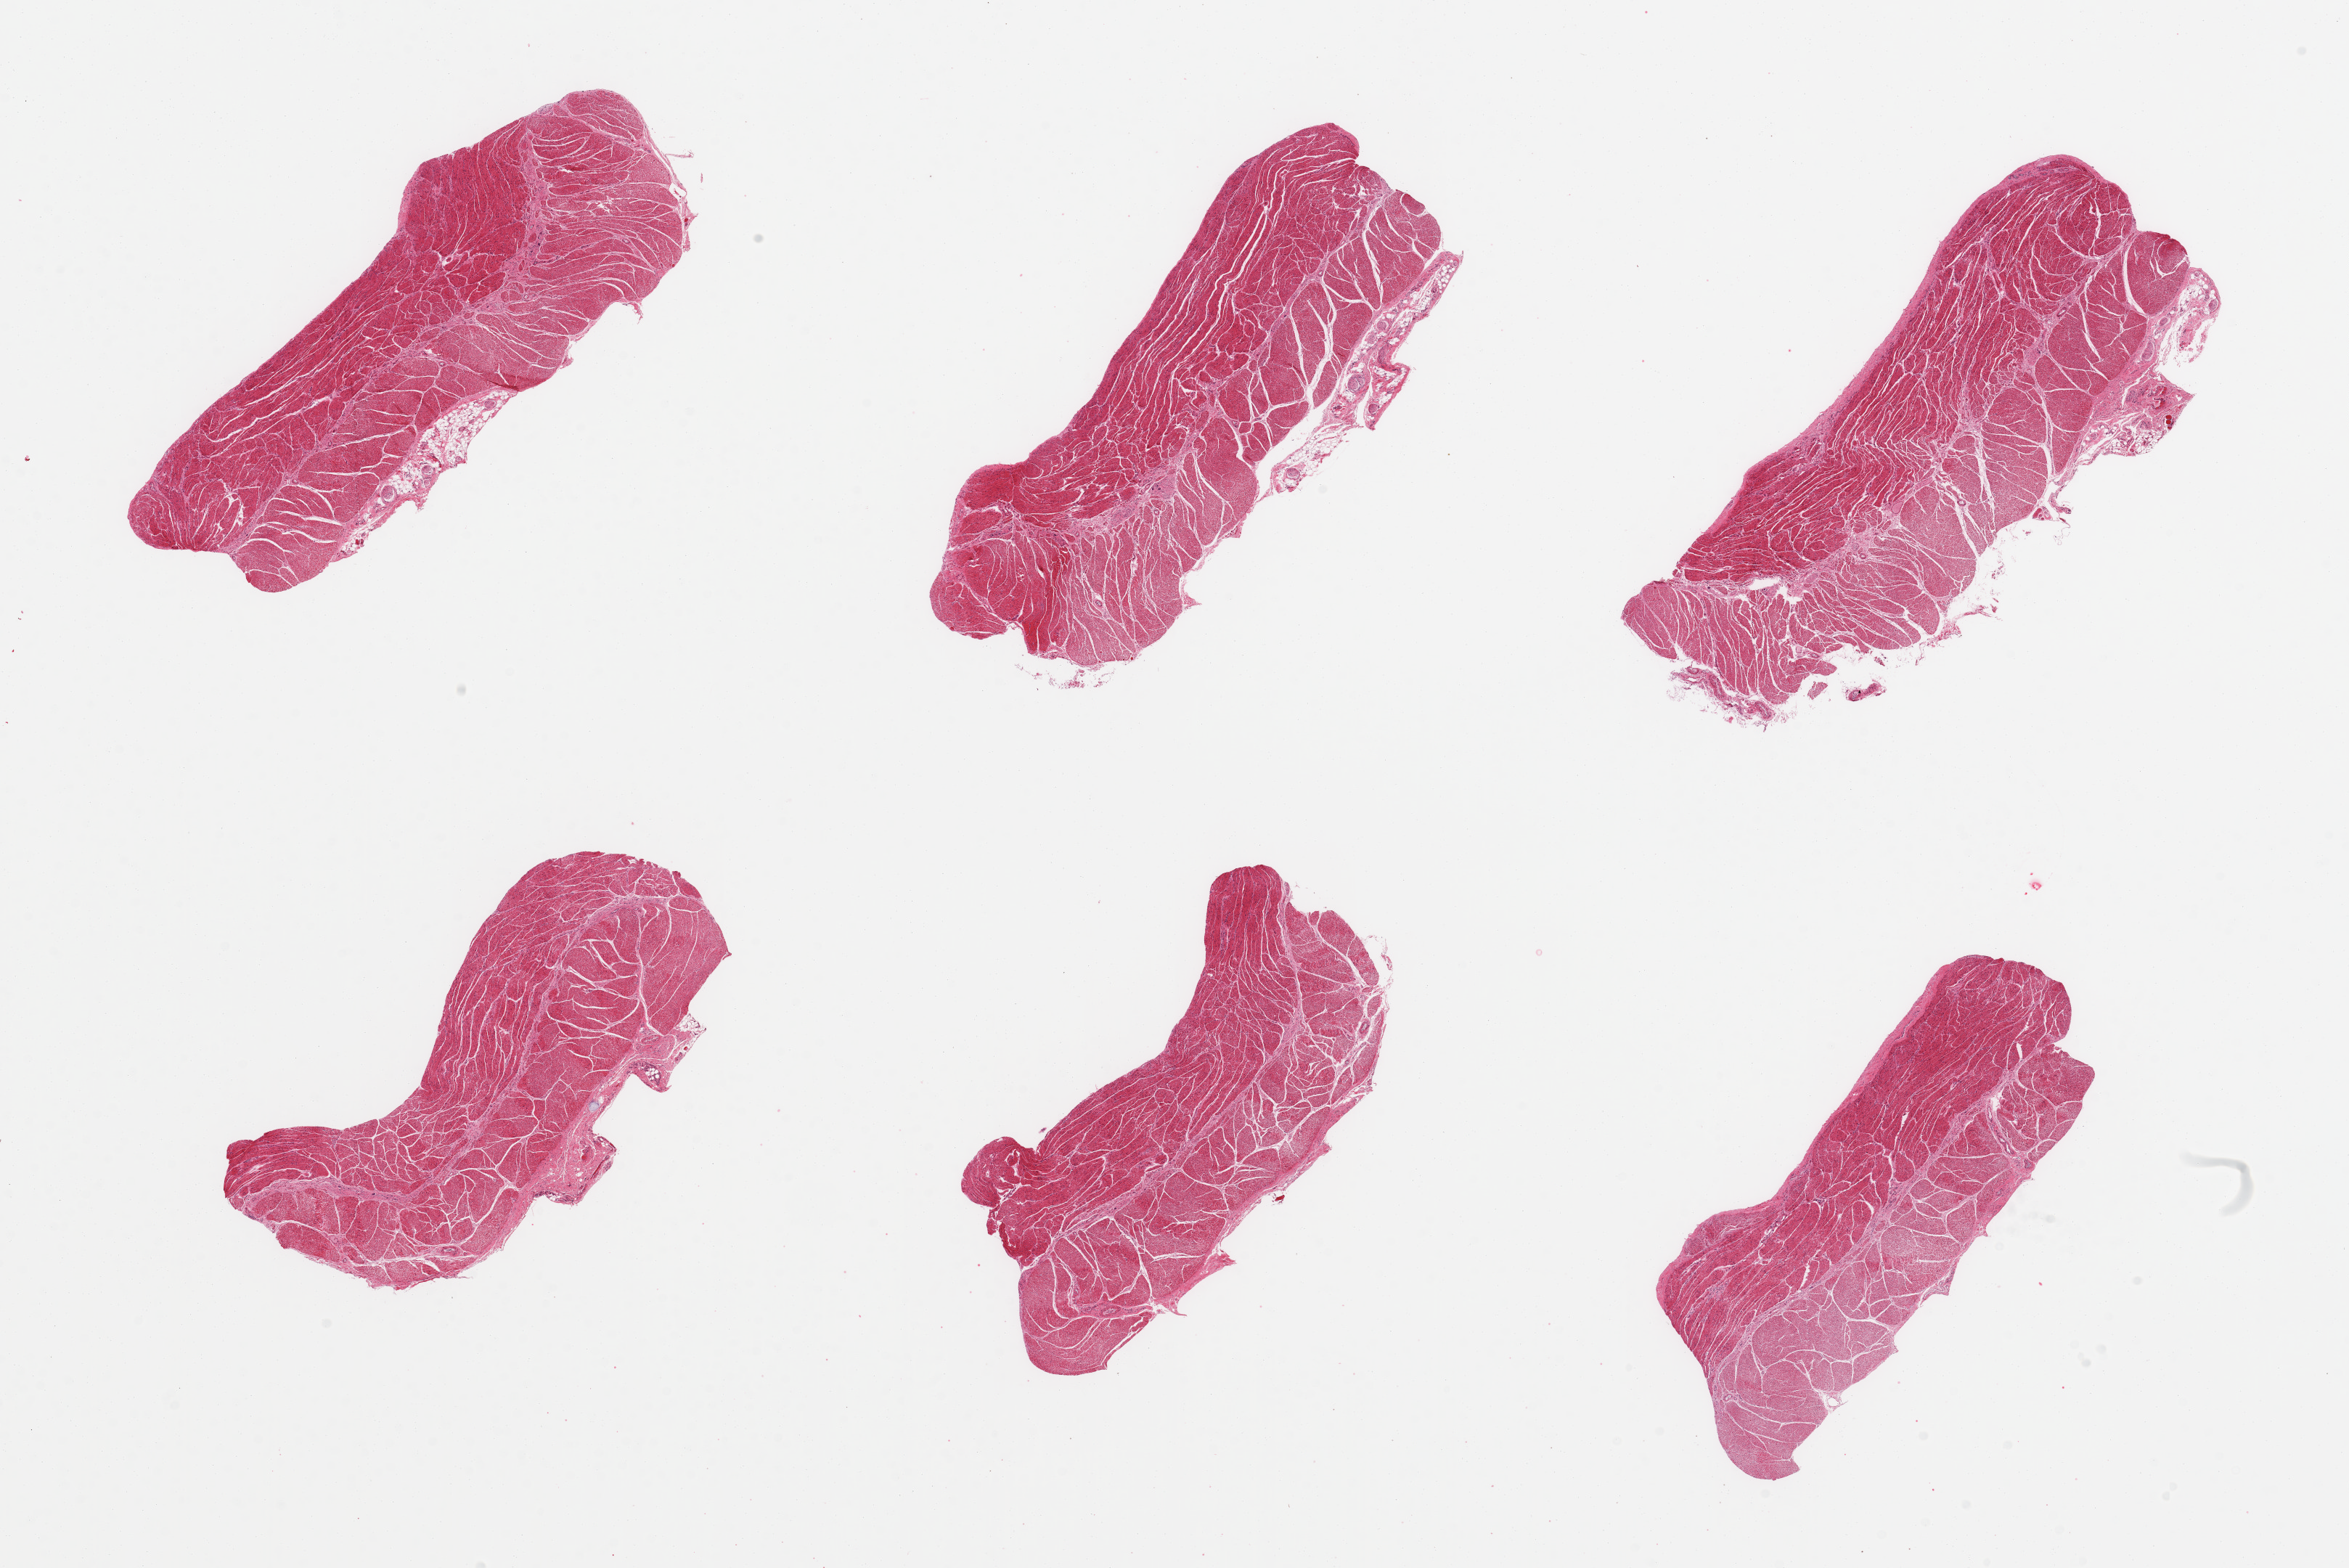
Whole-slide image, haematoxylin and eosin stain — whole scanned area (about 25.6 x 17.1 mm) shown as a low-resolution overview. PAXgene-fixed paraffin-embedded (PFPE) section. Target tissue: esophageal muscle. Tissue donor sample. Donor sex: female.
Pathologist's review note for this sample: 6 pieces; target muscularis, small amount of residual attached fat/nerve.